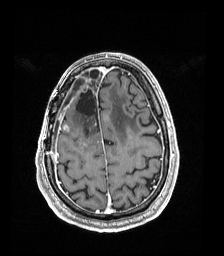
Brain MRI from a brain-tumour surgery series, one axial slice; position 48 of 192 along the scan axis; T1-weighted post-contrast; 1 mm slice thickness; 224 × 256 image matrix, field of view 224 × 256 mm. Case-level facts recorded for this patient, not image findings: histopathology: Astrocytoma; WHO grade: 4; IDH mutation: yes; tumour location: Right Frontal.
Annotated regions visible in this slice (manually delineated by an expert):
- previous resection cavity: bounding box <76,89,97,118> (left, top, right, bottom; pixels)
- tumour: <85,84,87,86>